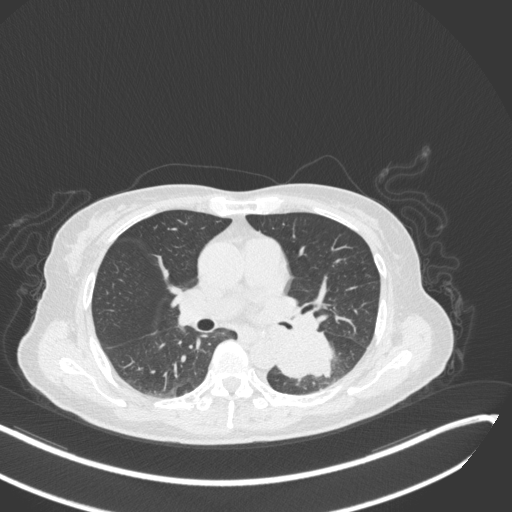
Chest CT, one axial slice; slice 152 of 342 in the series (ordered by position); 120 kVp; lung window (W 1500 / L -600 HU); 1 mm slice thickness; 512 × 512 image matrix. Patient: female, 64 years. From the clinical record (not read from this slice): clinical TNM (as recorded): T3 N1 M1.
Outlined on this slice (bounding box drawn by a radiologist):
- lung tumour (recorded histology: small cell carcinoma): box from (x=273, y=332) to (x=335, y=388) px